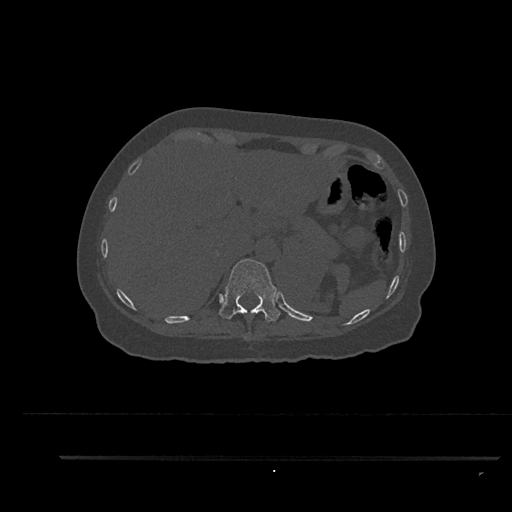
CT including the spine, one axial slice; slice 324 of 797 in the series (ordered by position); reconstruction kernel Br40s/3; 120 kVp; bone window (W 1800 / L 400 HU); 0.5 mm slice thickness; 512 × 512 image matrix, field of view 408 × 408 mm. Female patient, age 44 years. Case-level facts recorded for this patient, not image findings: primary cancer: renal.
Structures marked on this image (semi-automatic segmentation, software-assisted and operator-edited):
- T11 vertebra: box from (x=218, y=259) to (x=280, y=322) px